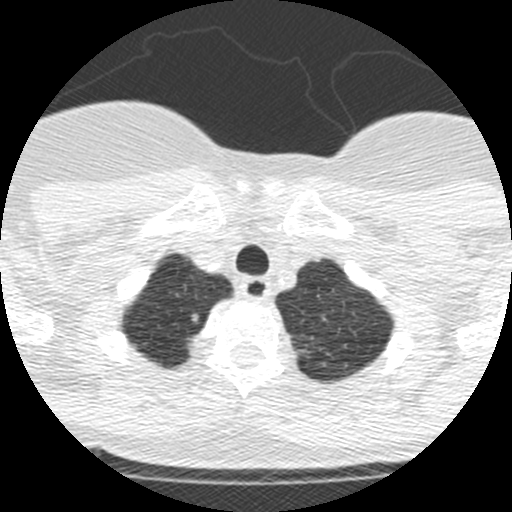
Low-dose screening chest CT, one axial slice. Position 219 of 250 along the scan axis. Reconstruction kernel STANDARD. 120 kVp. Lung window (W 1500 / L -600 HU). 1.25 mm slice thickness. 512 × 512 image matrix, field of view 257 × 257 mm.
Structures marked on this image (expert manual segmentation):
- lesion 1 (tumor, upper lobe of right lung): bounding box <192,314,199,322> (left, top, right, bottom; pixels)